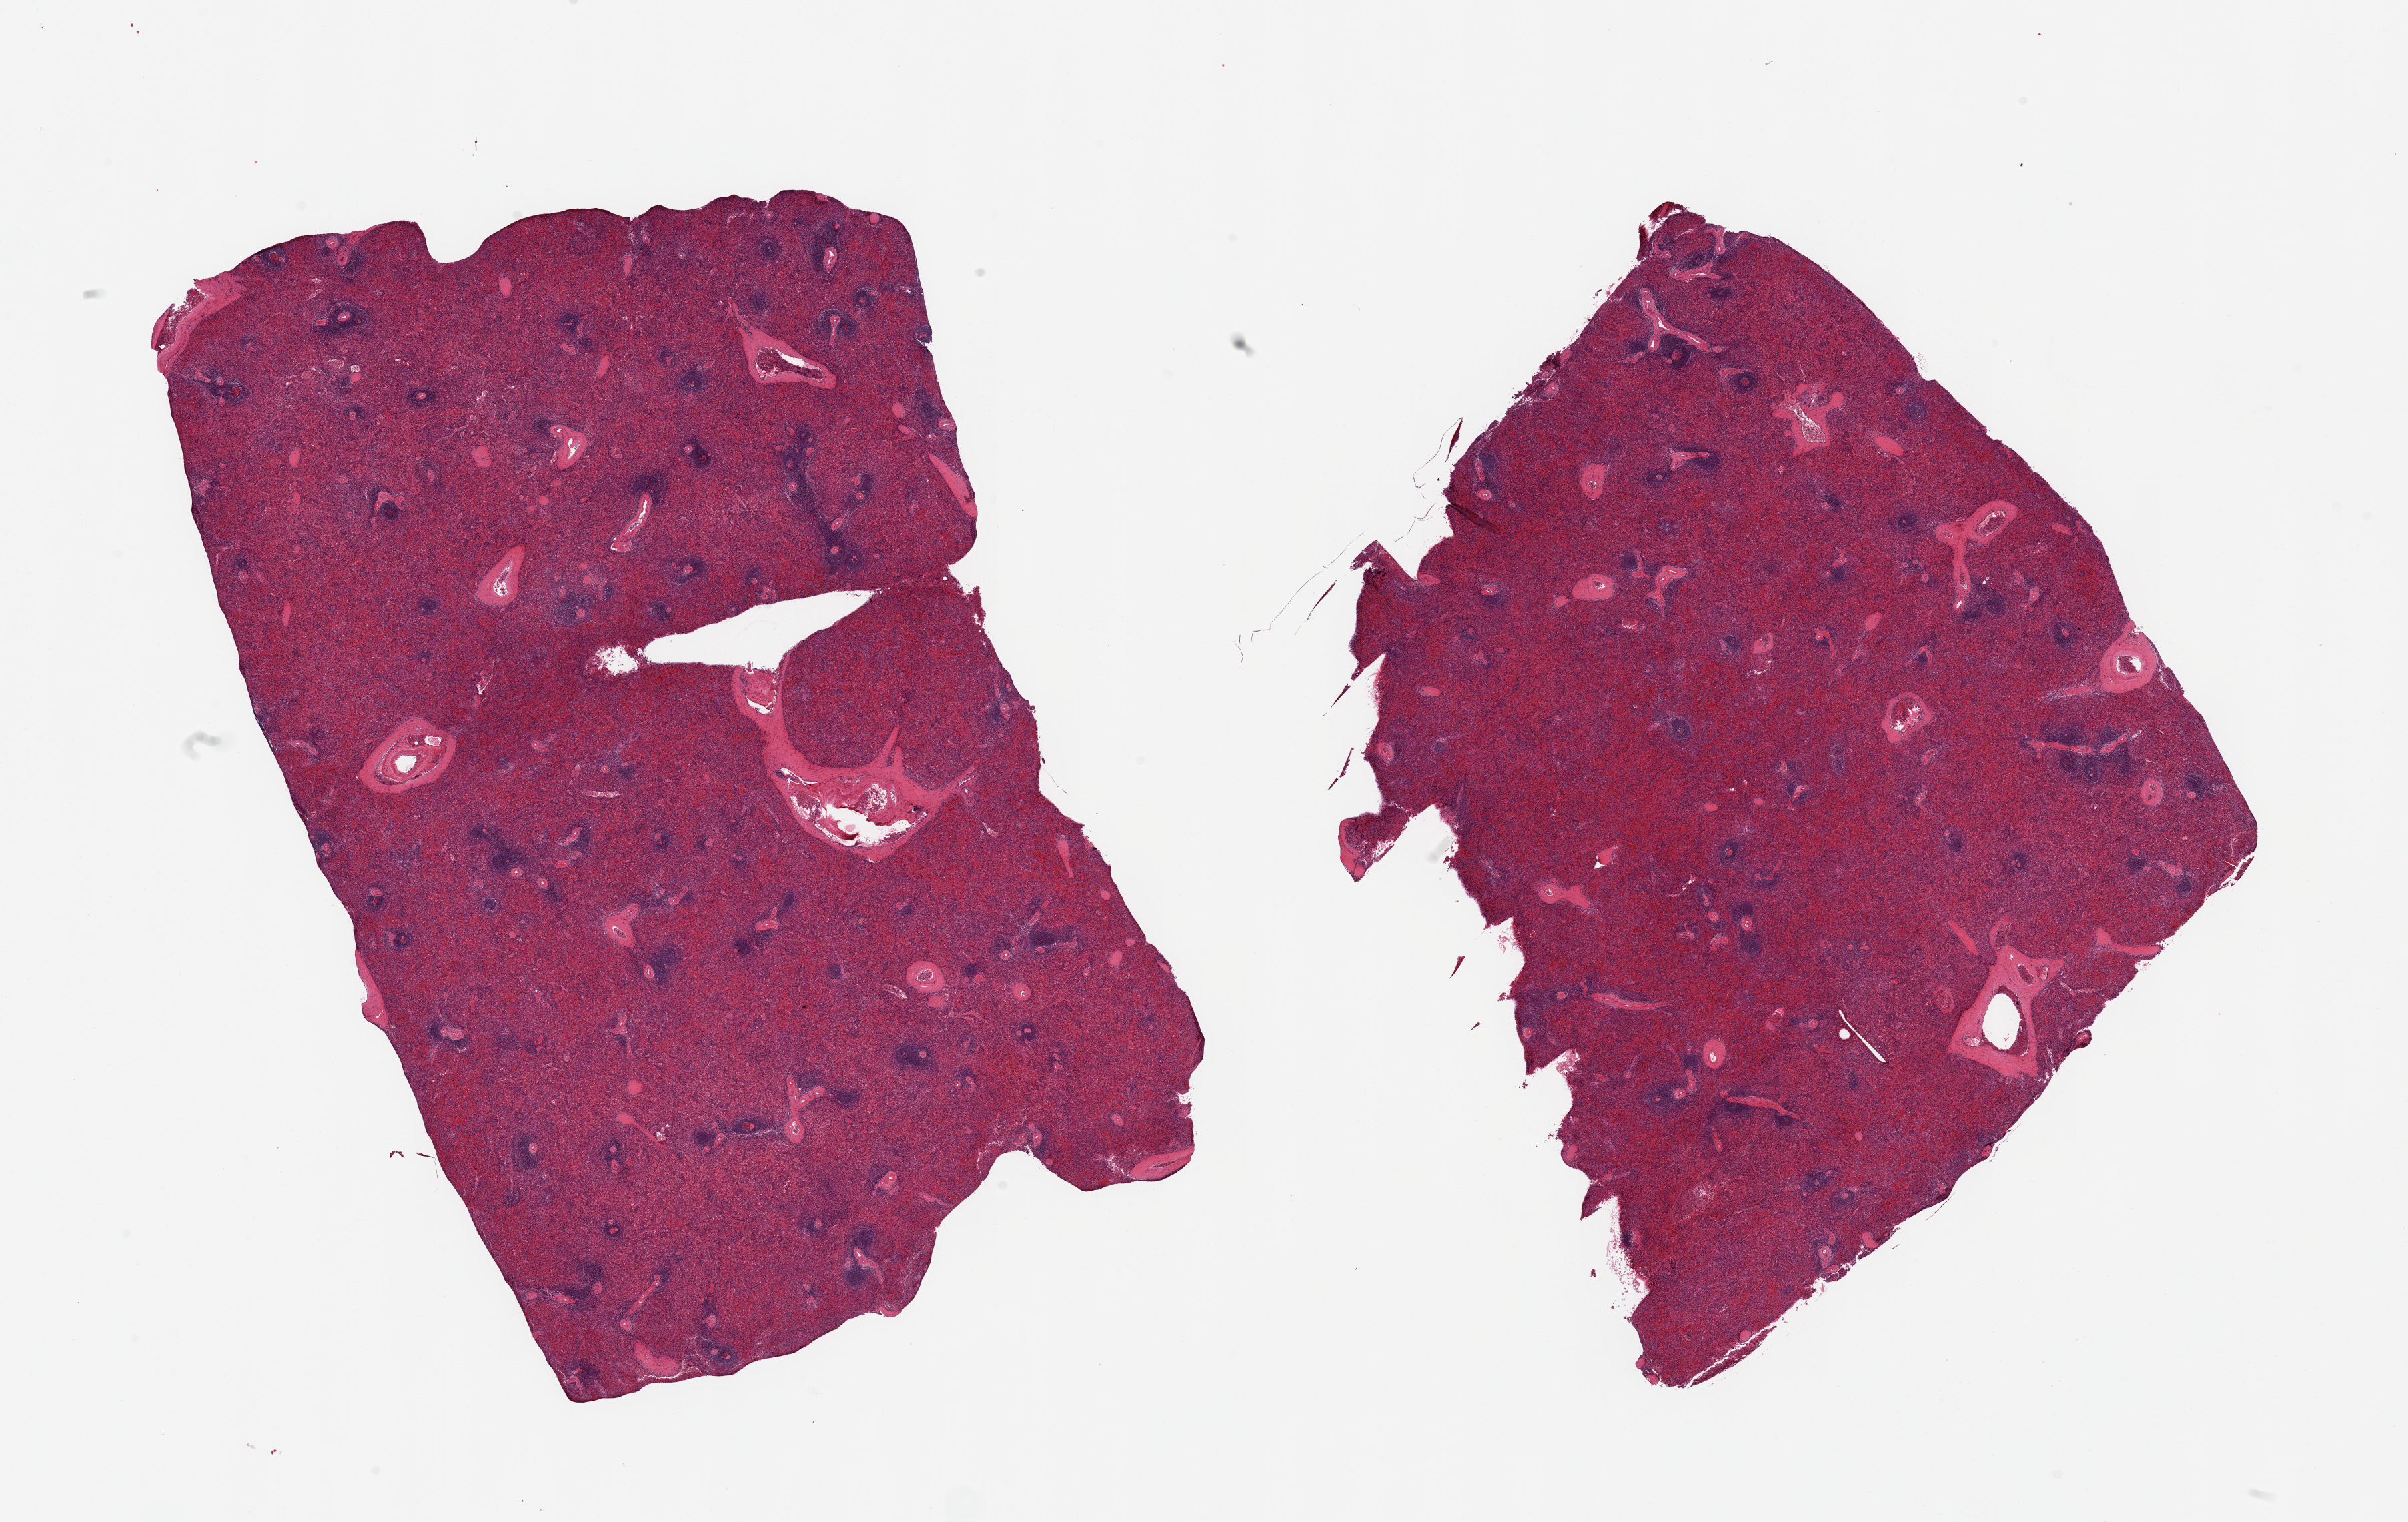
Hematoxylin and eosin (H&E) whole-slide image, brightfield, whole scanned area (about 28.5 x 18.0 mm, from a 20x scan) shown as a low-resolution overview. PAXgene-fixed paraffin-embedded (PFPE) section. Section of spleen (target tissue). Donor tissue sample. Donor: male.
Reviewer comment on this tissue sample: 2 pieces; moderately congested.